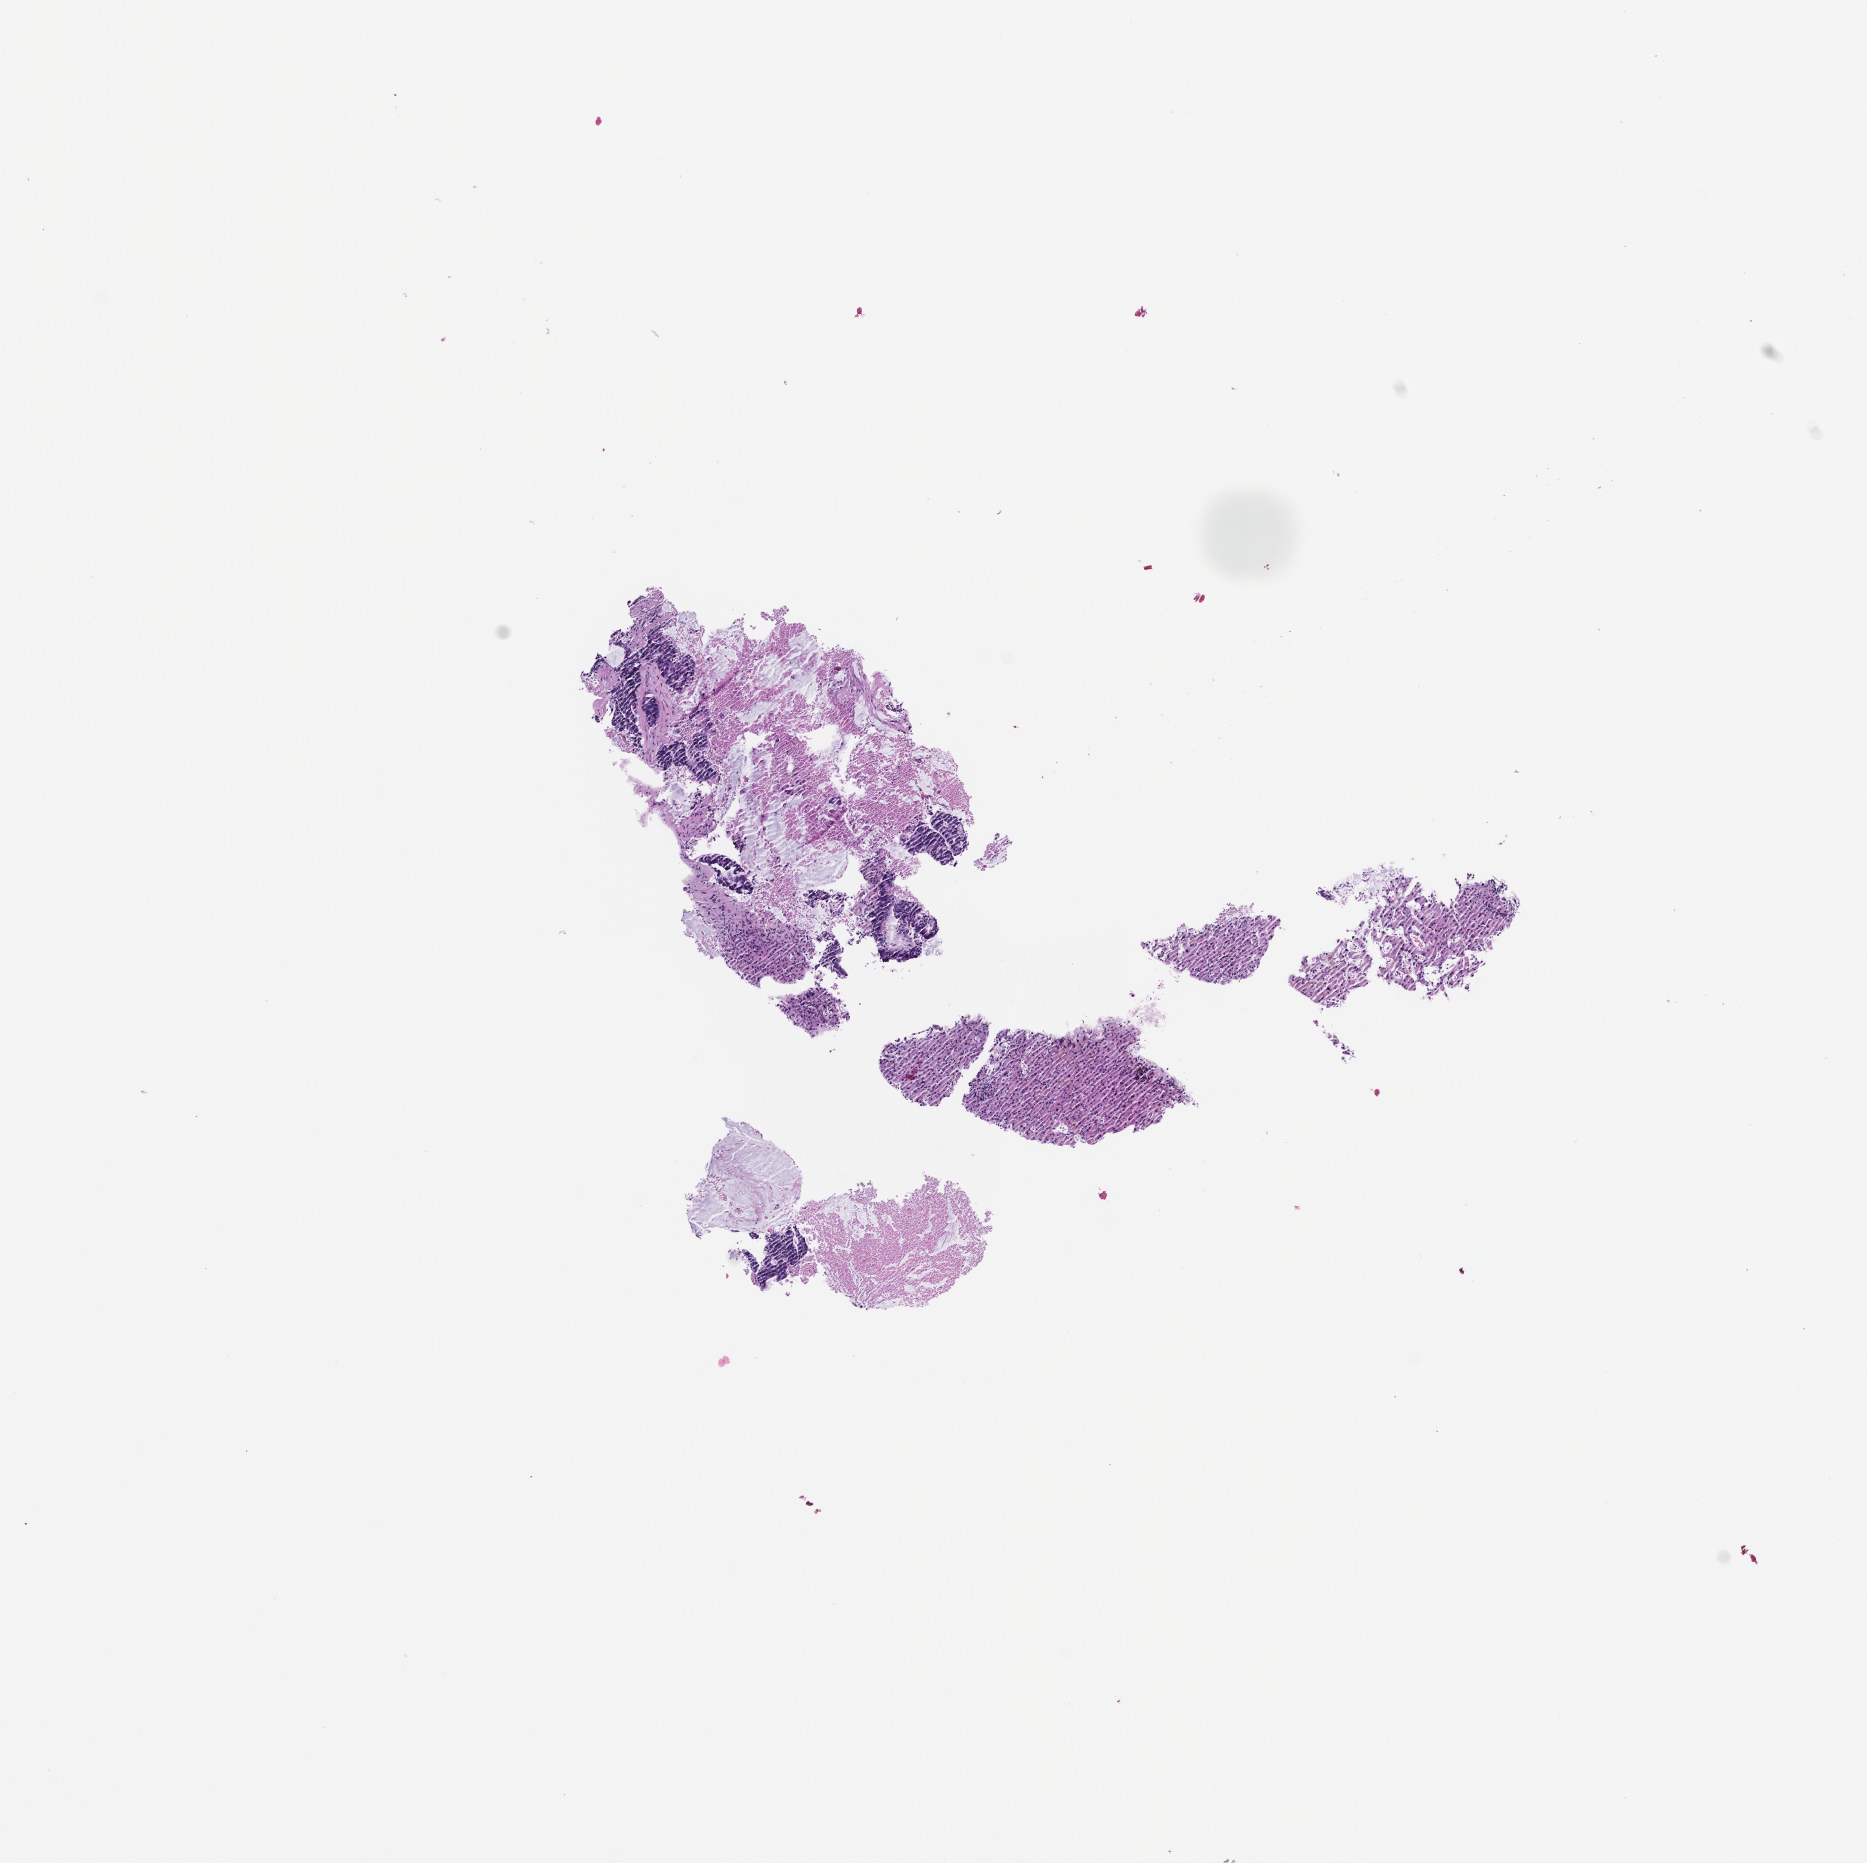
Digitized hematoxylin and eosin (H&E)-stained section, shown as a low-resolution overview of the whole scanned area (about 7.5 x 7.5 mm). Formalin-fixed paraffin-embedded section. Collected at baseline (before treatment). Patient: female.
* this section: metastasis (sampled organ not recorded)
* primary diagnosis of the patient: Colorectal Carcinoma